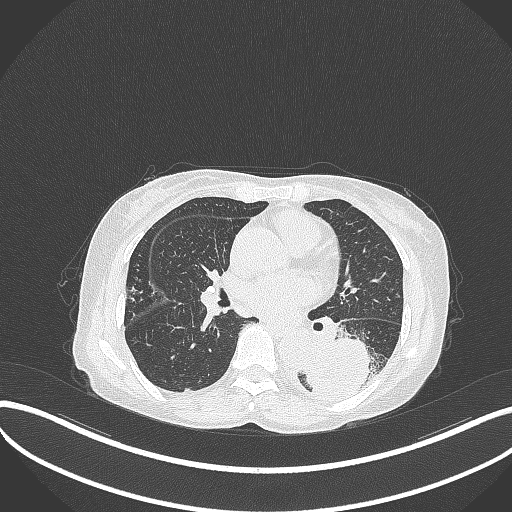
Chest CT, one axial slice; slice 155 of 370 in the series (ordered by position); lung window (W 1500 / L -600 HU); 512 × 512 image matrix, field of view 400 × 400 mm. Female patient, age 78 years. Case-level facts recorded for this patient, not image findings: clinical TNM (as recorded): T3 N0 M1.
Annotated regions visible in this slice (bounding box drawn by a radiologist):
- lung tumour (recorded histology: squamous cell carcinoma): bounding box (x1, y1, x2, y2) in pixels: (306, 328, 390, 402)